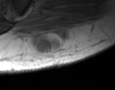
MRI of an extremity soft-tissue mass, one axial slice. Position 12 of 35 along the scan axis. MR volume resampled by the dataset authors to the PET/CT grid (not the native acquisition matrix). 115 × 90 image matrix, field of view 112 × 88 mm. Male patient. From the clinical record (not read from this slice): histological type: pleiomorphic leiomyosarcoma; grade: high; site of the primary tumour: left buttock.
Annotated regions visible in this slice (expert contour drawn on MRI and transferred to this co-registered scan by the dataset authors):
- gross tumour volume including surrounding oedema: box from (x=33, y=28) to (x=70, y=54) px
- gross tumour volume (mass): (x=39, y=33)–(x=68, y=53)